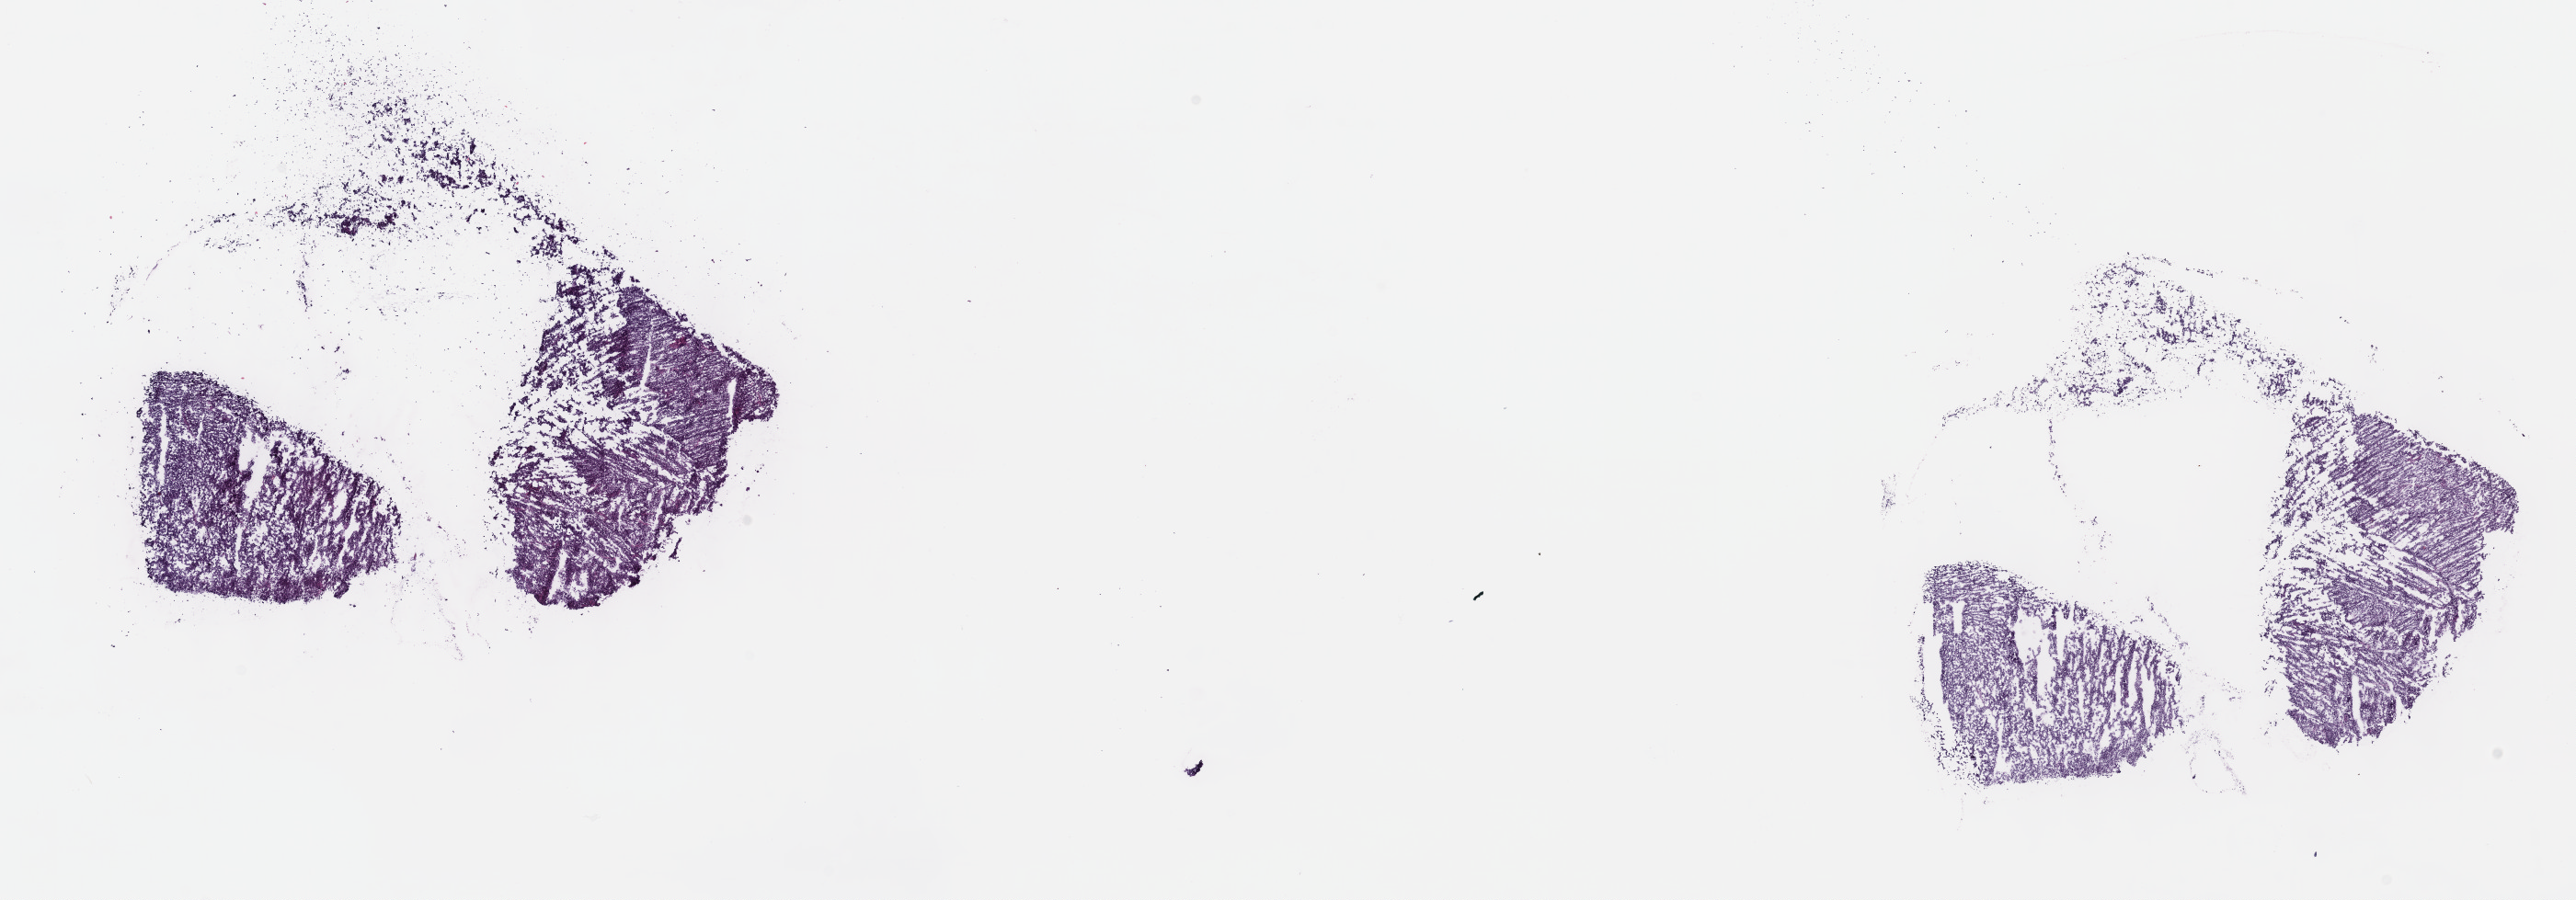
Digitized Hematoxylin and eosin (H&E) stained tissue section (whole slide), low-resolution overview of the scanned area, about 22.7 x 7.9 mm, frozen section, sample: primary tumour, uvea. Male patient; age at initial diagnosis 64 years. Slide review estimates, as recorded: tumour cells 85%, tumour nuclei 85%, normal cells 0%, stromal cells 15%, necrosis 0%. Inflammatory infiltration, as recorded: lymphocyte infiltration 0%, monocyte infiltration 0%, neutrophil infiltration 0%.
TNM: T3a N0 M0. Laterality: right. Histologic diagnosis: Spindle cell melanoma, type B (choroid). AJCC pathologic stage: IIB (7th edition).